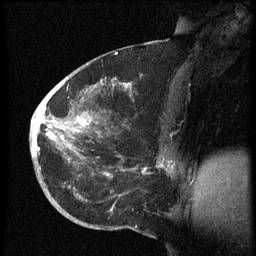
Breast MRI (dynamic contrast-enhanced), one sagittal slice. Slice 31 of 60 in the series (ordered by position). Dynamic contrast-enhanced series, image 2 of 3 at this slice position (ordered by acquisition). 1.5 T. TE 4.2 ms, TR 8.4 ms. 256 × 256 image matrix, field of view 200 × 200 mm. Female patient, age 38 years. Case-level facts recorded for this patient, not image findings: setting: breast cancer imaged before/during neoadjuvant chemotherapy; receptor status: HER2-positive.
Annotated regions visible in this slice (semi-automatic segmentation, software-assisted and operator-edited):
- analysis volume of interest (the breast-tissue region the enhancement analysis was run in; not a lesion): box from (x=30, y=74) to (x=173, y=202) px
- tumour enhancement mask (voxels above the 70 % enhancement threshold inside the analysis volume of interest): (x=32, y=84)–(x=173, y=176)